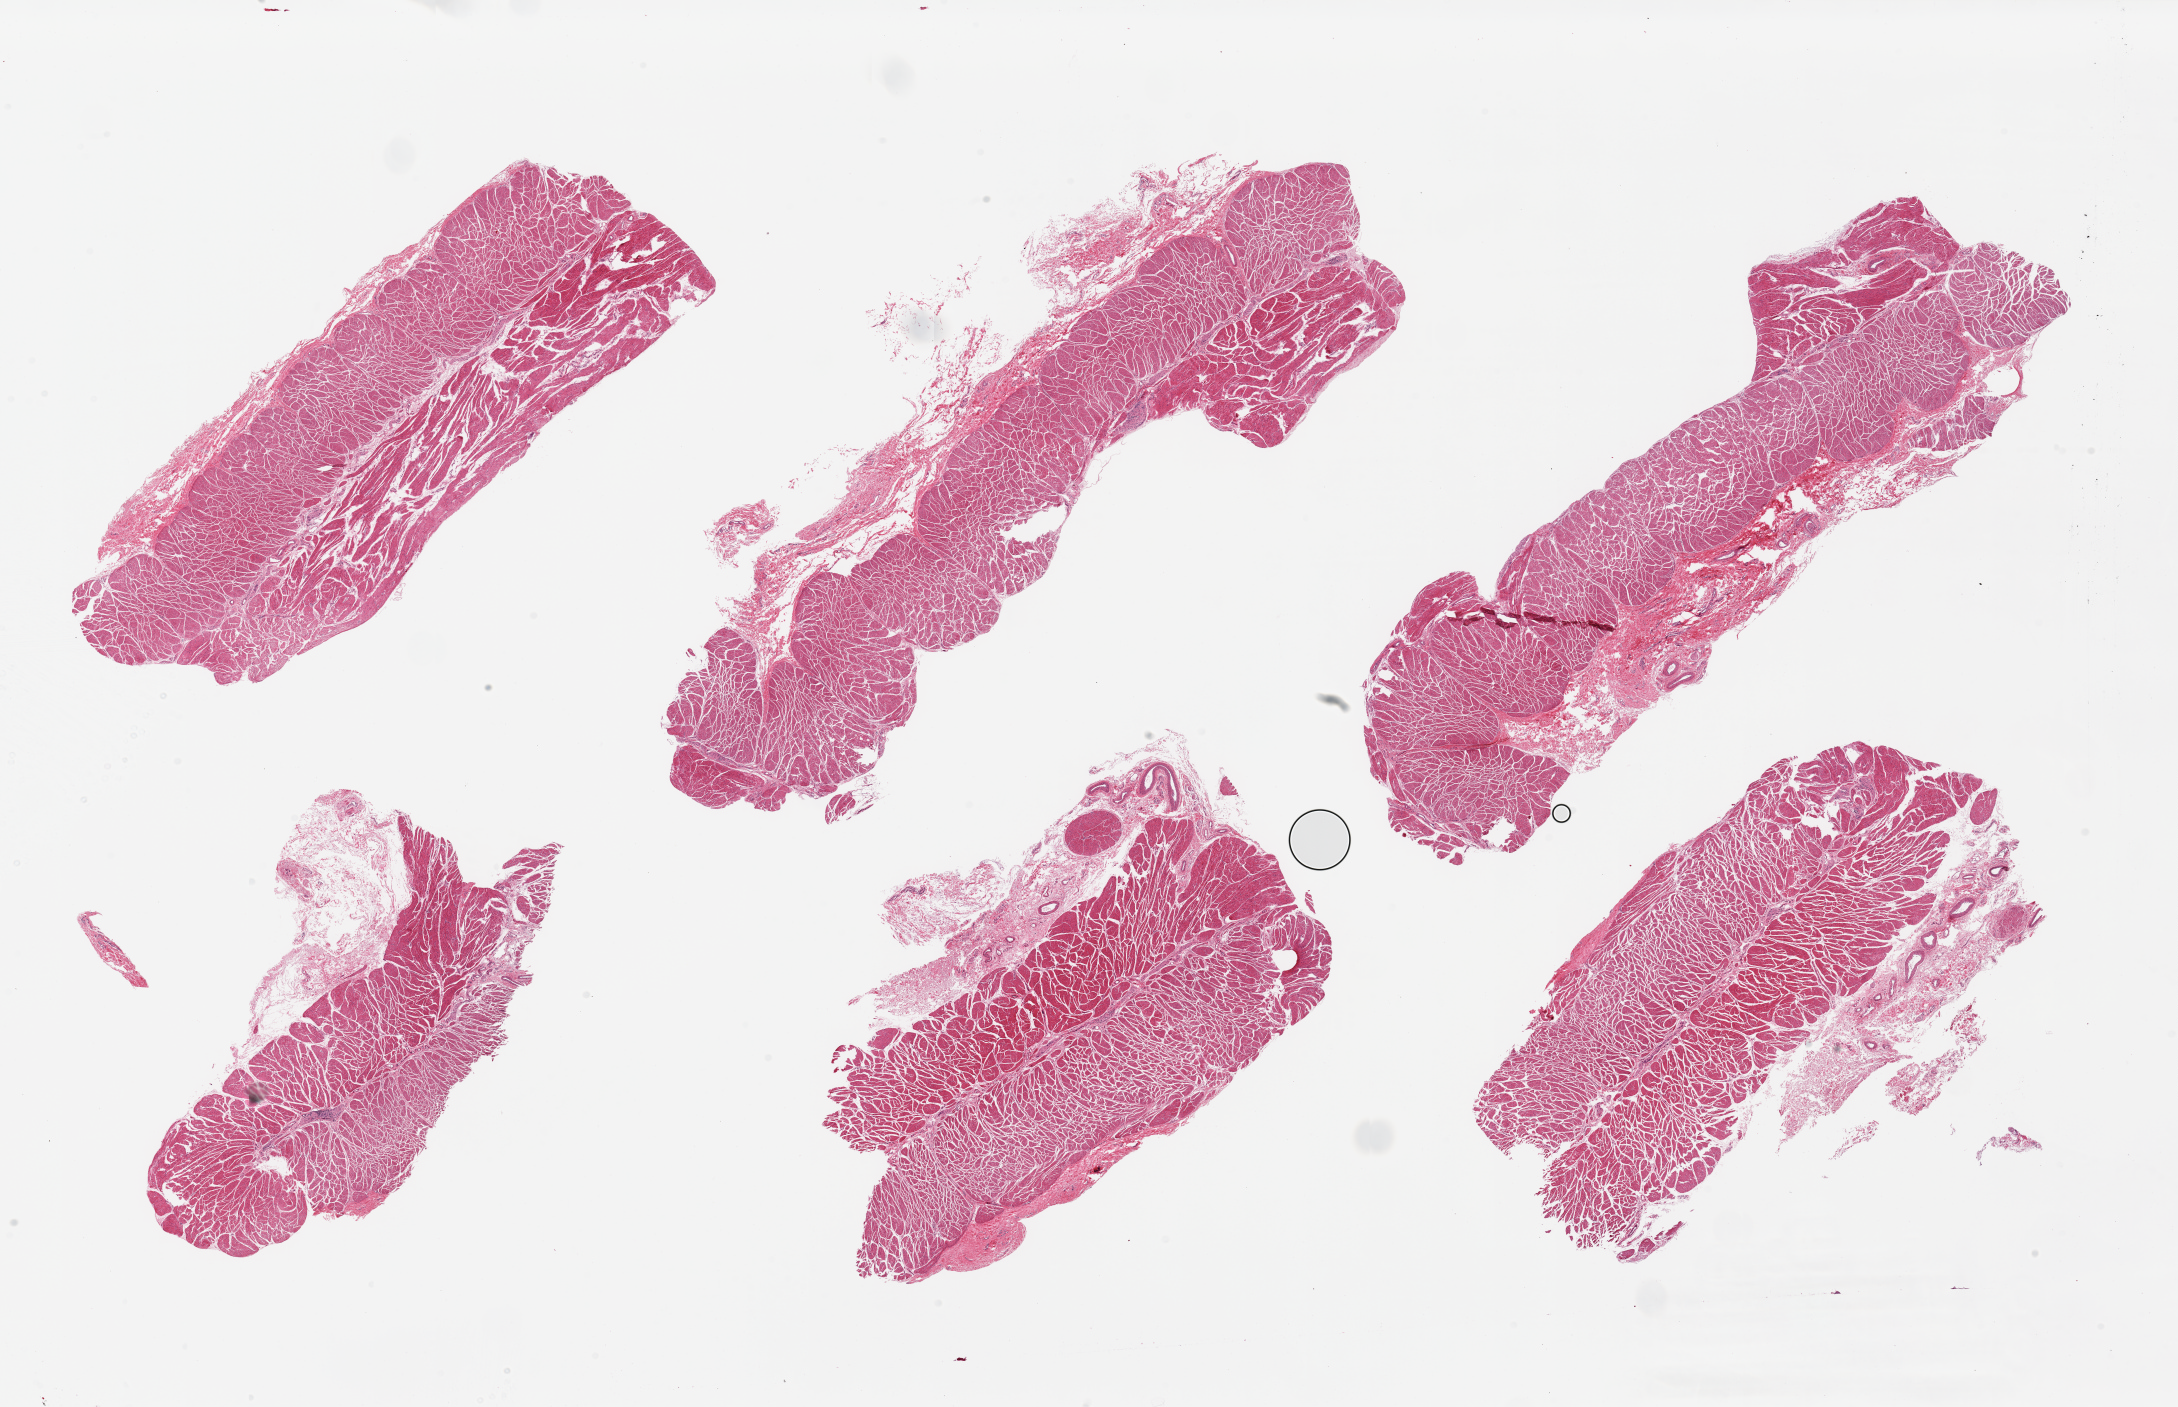
Whole-slide image, hematoxylin and eosin (H&E) stain, brightfield, low-resolution overview of the scanned area, about 34.5 x 22.3 mm (from a 20x scan); PAXgene-fixed paraffin-embedded (PFPE) section; section of gastroesophageal junction (target tissue); tissue donor sample. Donor sex: female.
Review note (as recorded): 6 pieces, up to 14x6mm; all muscuarlis; good specimens.